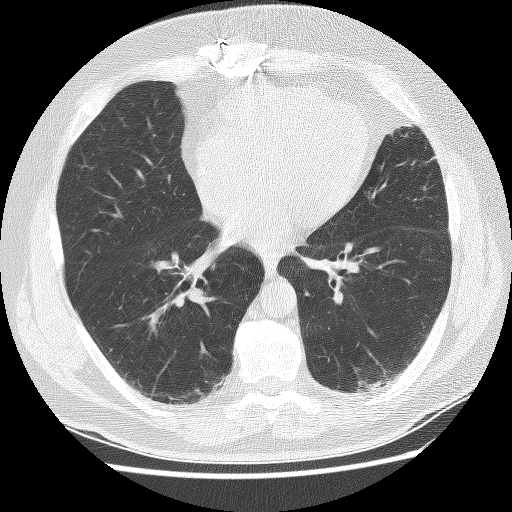
Low-dose screening chest CT, axial slice, baseline screening round, lung window (W 1500 / L -600 HU), 2.5 mm slice thickness, 120 kVp. Male participant, aged 65 years at enrolment. Former smoker at enrolment.
Lesion marked by an expert reader, bounding box <353,371,394,406> (left, top, right, bottom; pixels). Screening reader's record for this exam: no non-calcified nodule ≥4 mm recorded. Official screen result: negative screen, minor abnormalities not suspicious for lung cancer. Later outcome: lung cancer diagnosed 523 days after this screen (after the second annual screen) — squamous cell carcinoma, NOS, left lower lobe, moderately differentiated (G2), stage IA (AJCC 6th edition), 20 mm at pathology.